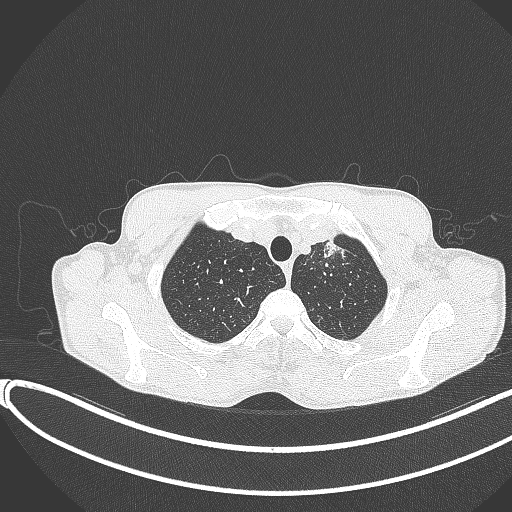
Chest CT, one axial slice; position 336 of 374 along the scan axis; reconstruction kernel B70f; lung window (W 1500 / L -600 HU); 1 mm slice thickness; 512 × 512 image matrix. Patient: male, 58 years. Case-level facts recorded for this patient, not image findings: clinical TNM (as recorded): T1c N1 M0.
Outlined on this slice (rectangle marked by the reading radiologist):
- lung tumour (recorded histology: adenocarcinoma): bounding box (x1, y1, x2, y2) in pixels: (316, 230, 345, 262)